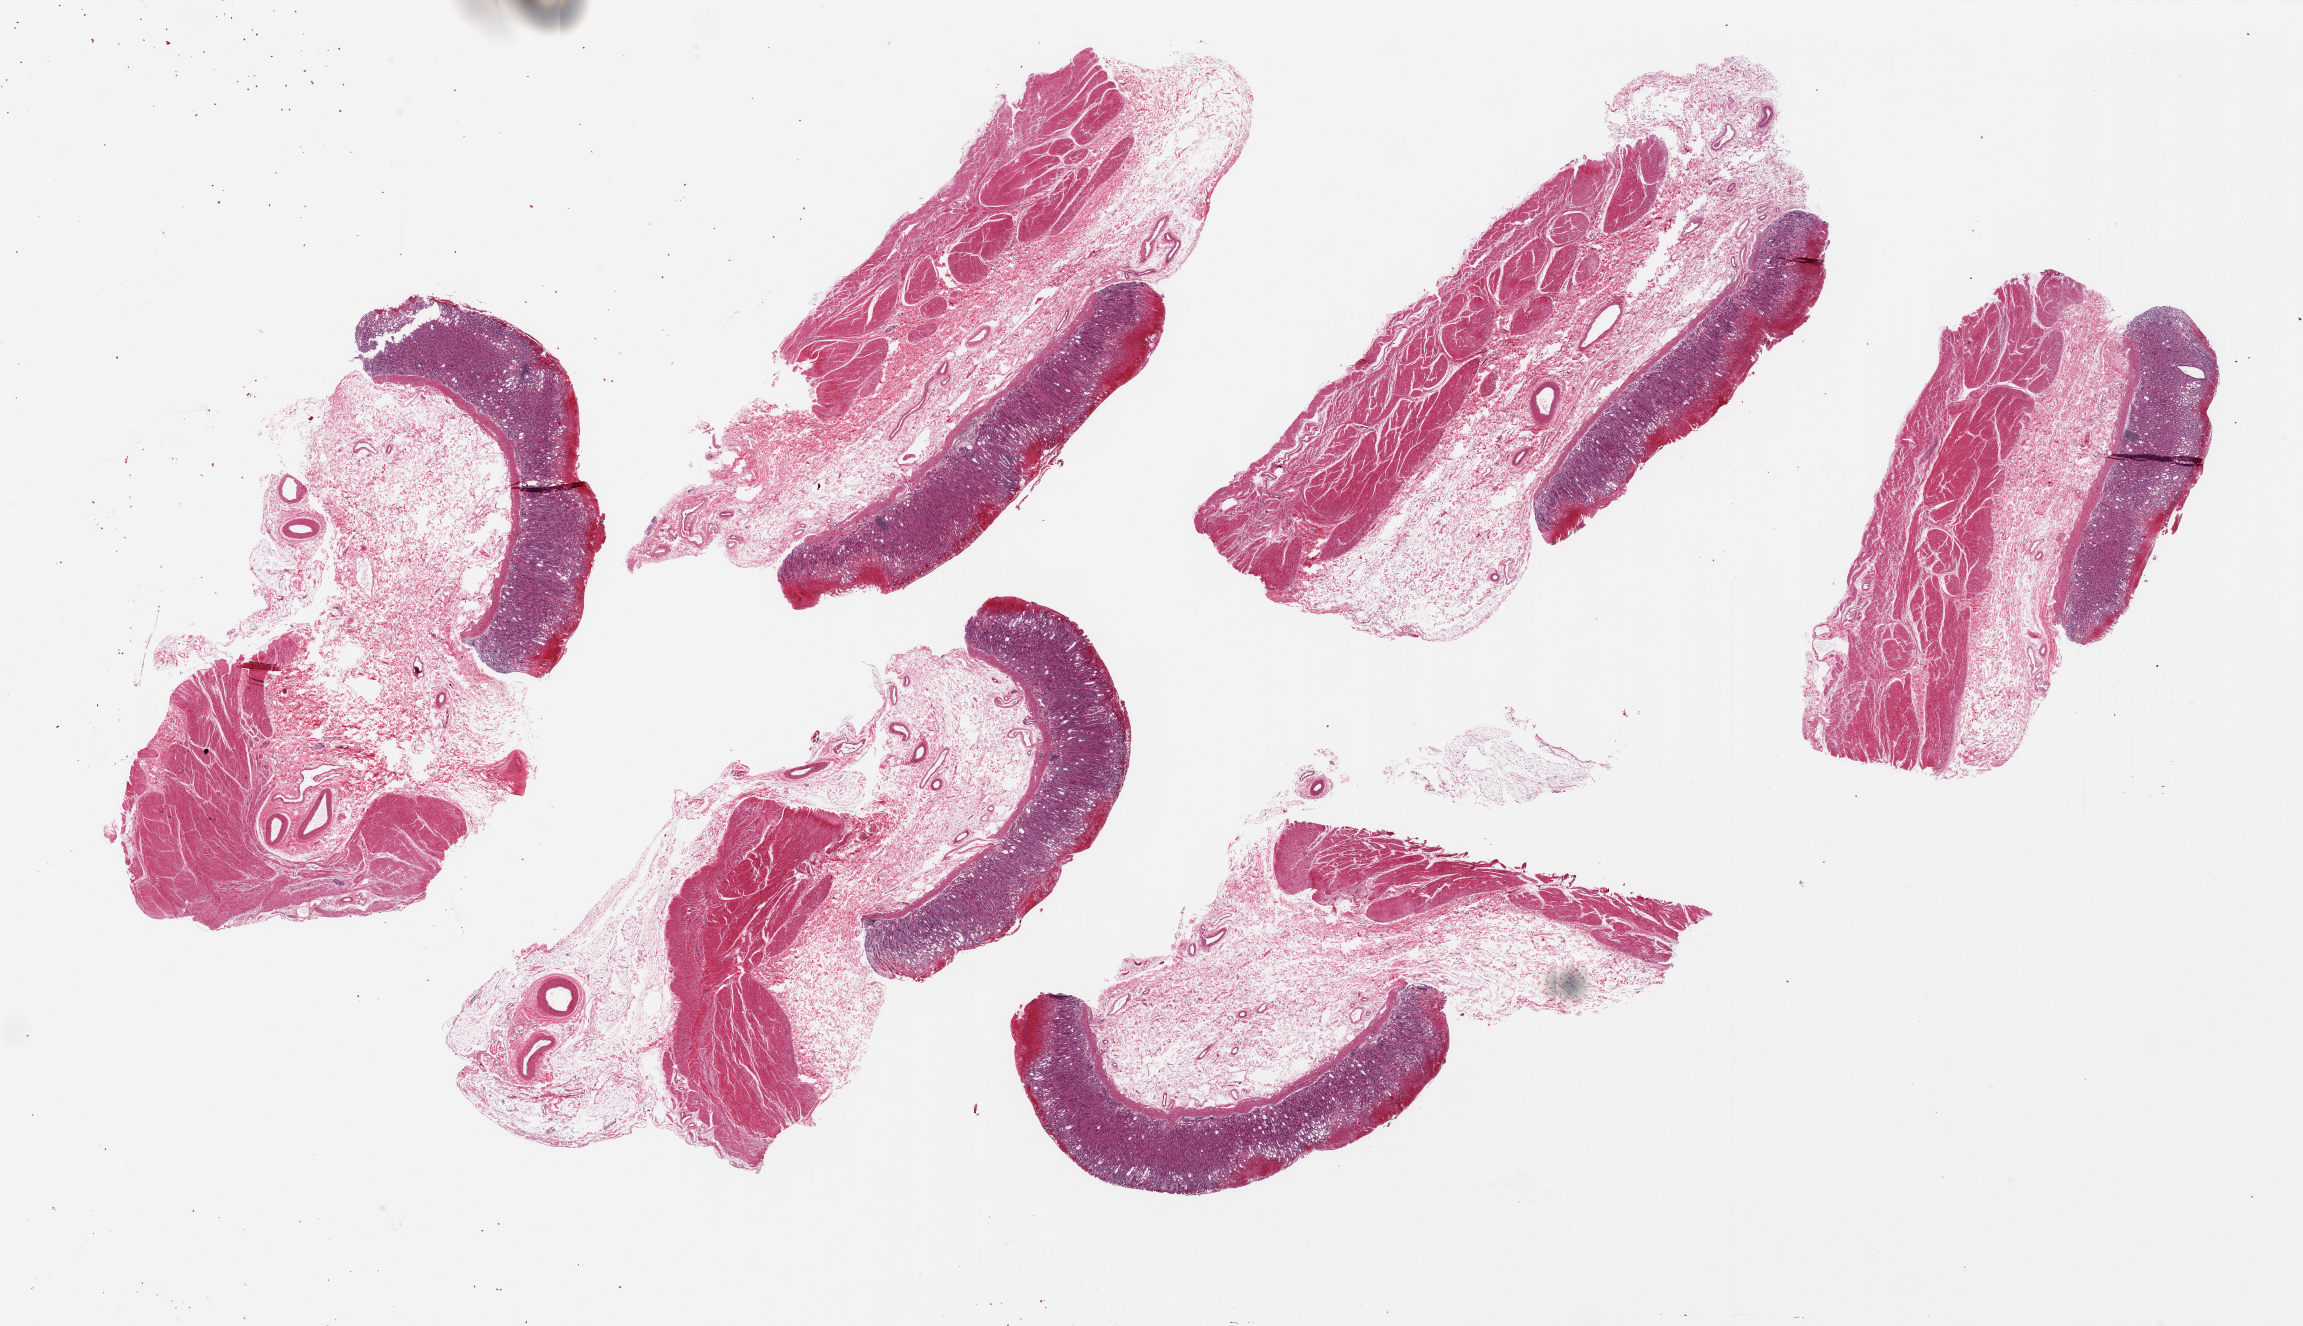
H&E whole-slide image — low-resolution overview of the scanned area, about 36.4 x 21.0 mm. PAXgene-fixed, paraffin-embedded tissue. Target tissue: stomach. Tissue donor sample. Donor: male.
Reviewer comment on this tissue sample: 6 pieces, ~10x4mm. Mucosa well- preserved, ~20-25% of thickness. Surface hemorrhage/erosions ? etiology.